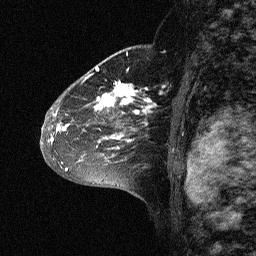
Breast MRI (dynamic contrast-enhanced), one sagittal slice; position 41 of 64 along the scan axis; dynamic contrast-enhanced study with each time point stored as its own series, time point 2 of 3 at this slice position (early post-contrast, ordered by acquisition time); 1.5 T; TE 4.5 ms, TR 11 ms; 256 × 256 image matrix, field of view 200 × 200 mm. Patient: female, 46 years. Case-level facts recorded for this patient, not image findings: setting: breast cancer imaged before/during neoadjuvant chemotherapy; receptor status: HER2-positive.
Annotated regions visible in this slice (semi-automatic segmentation, software-assisted and operator-edited):
- analysis volume of interest (the breast-tissue region the enhancement analysis was run in; not a lesion): bounding box (x1, y1, x2, y2) in pixels: (43, 72, 164, 177)
- tumour enhancement mask (voxels above the 90 % enhancement threshold inside the analysis volume of interest): (48, 72, 162, 171)